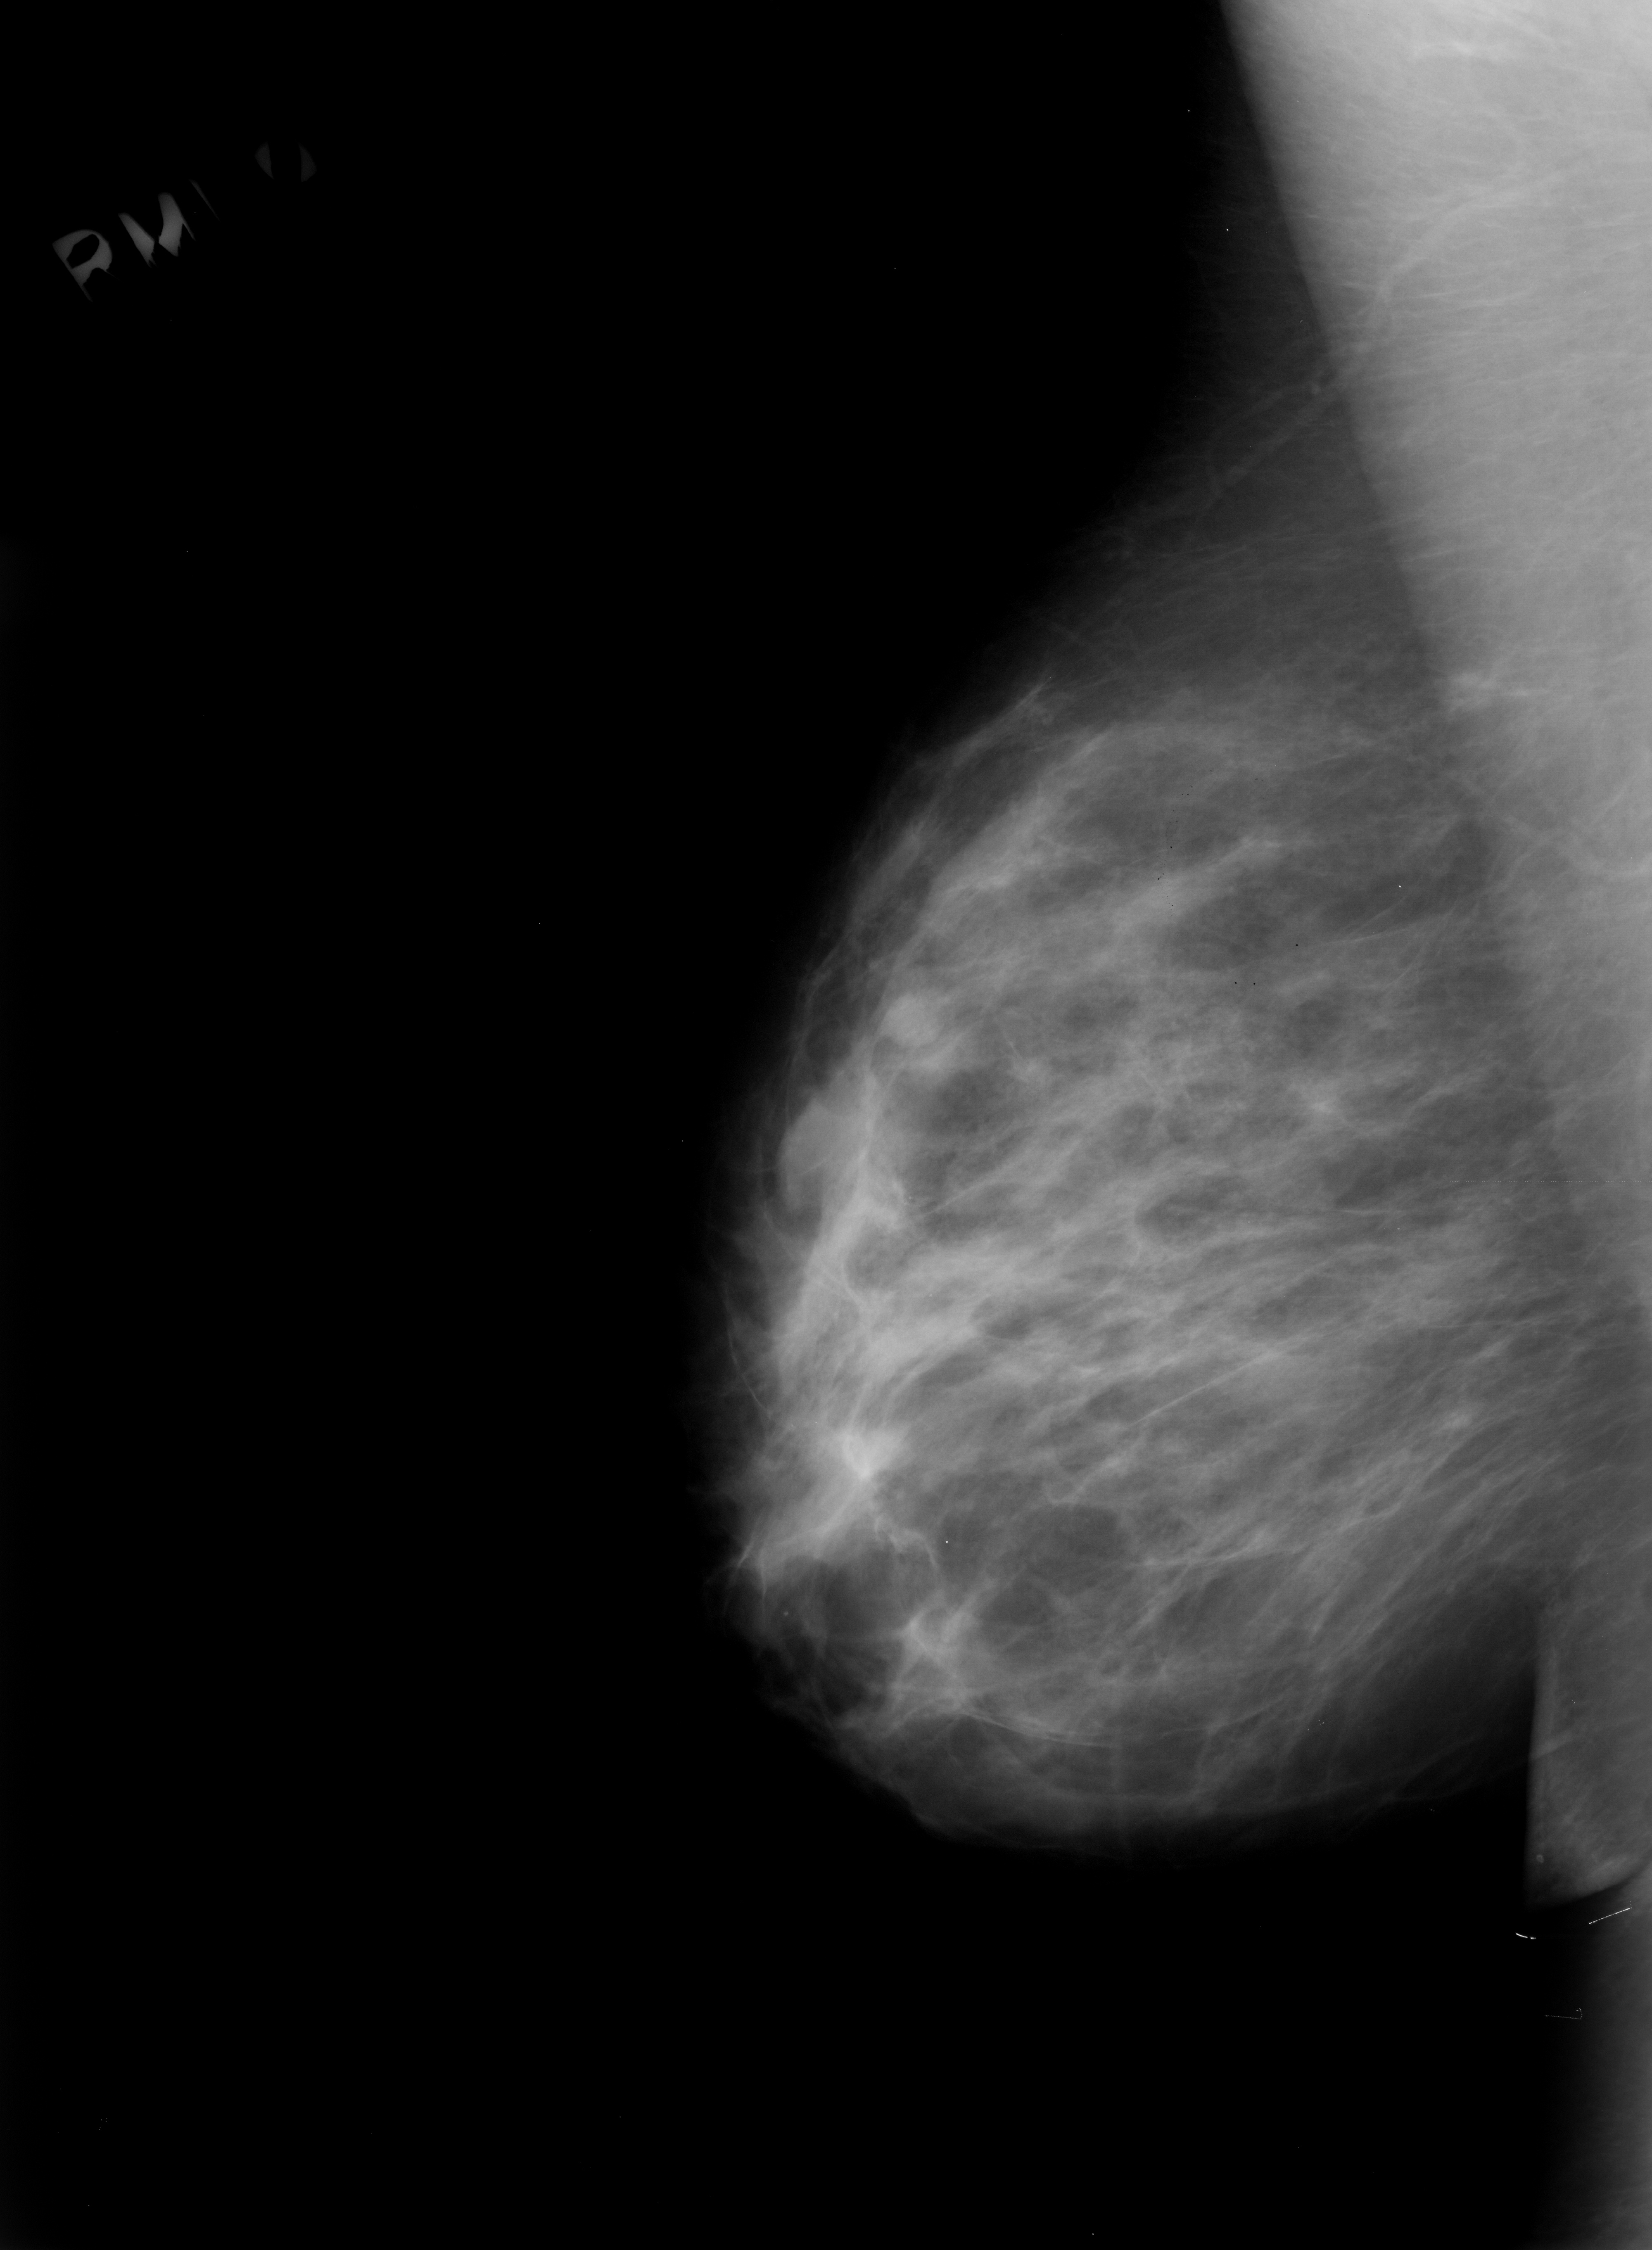
Mammogram (digitized film). Right breast. Mediolateral oblique (MLO) view. Breast composition: scattered fibroglandular densities (BI-RADS density category 2 of 4). 1652 × 2250 image matrix.
Expert-marked regions of interest on this film, with their recorded descriptors:
- mass, shape oval, margins circumscribed; BI-RADS assessment category 3; pathology result (as recorded, not read from the image): benign: bounding box [x1, y1, x2, y2] px = [868, 977, 978, 1090]